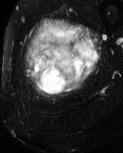
MRI of an extremity soft-tissue mass, one axial slice. T2-weighted fat-saturated. MR volume resampled by the dataset authors to the PET/CT grid (not the native acquisition matrix). 3.27 mm slice thickness. 123 × 153 image matrix, field of view 120 × 149 mm. Male patient. Case-level facts recorded for this patient, not image findings: histological type: pleiomorphic liposarcoma; grade: high; site of the primary tumour: left thigh.
Outlined on this slice (expert contour drawn on MRI and transferred to this co-registered scan by the dataset authors):
- gross tumour volume including surrounding oedema: bounding box [x1, y1, x2, y2] px = [27, 18, 101, 98]
- gross tumour volume (mass): [33, 49, 83, 94]